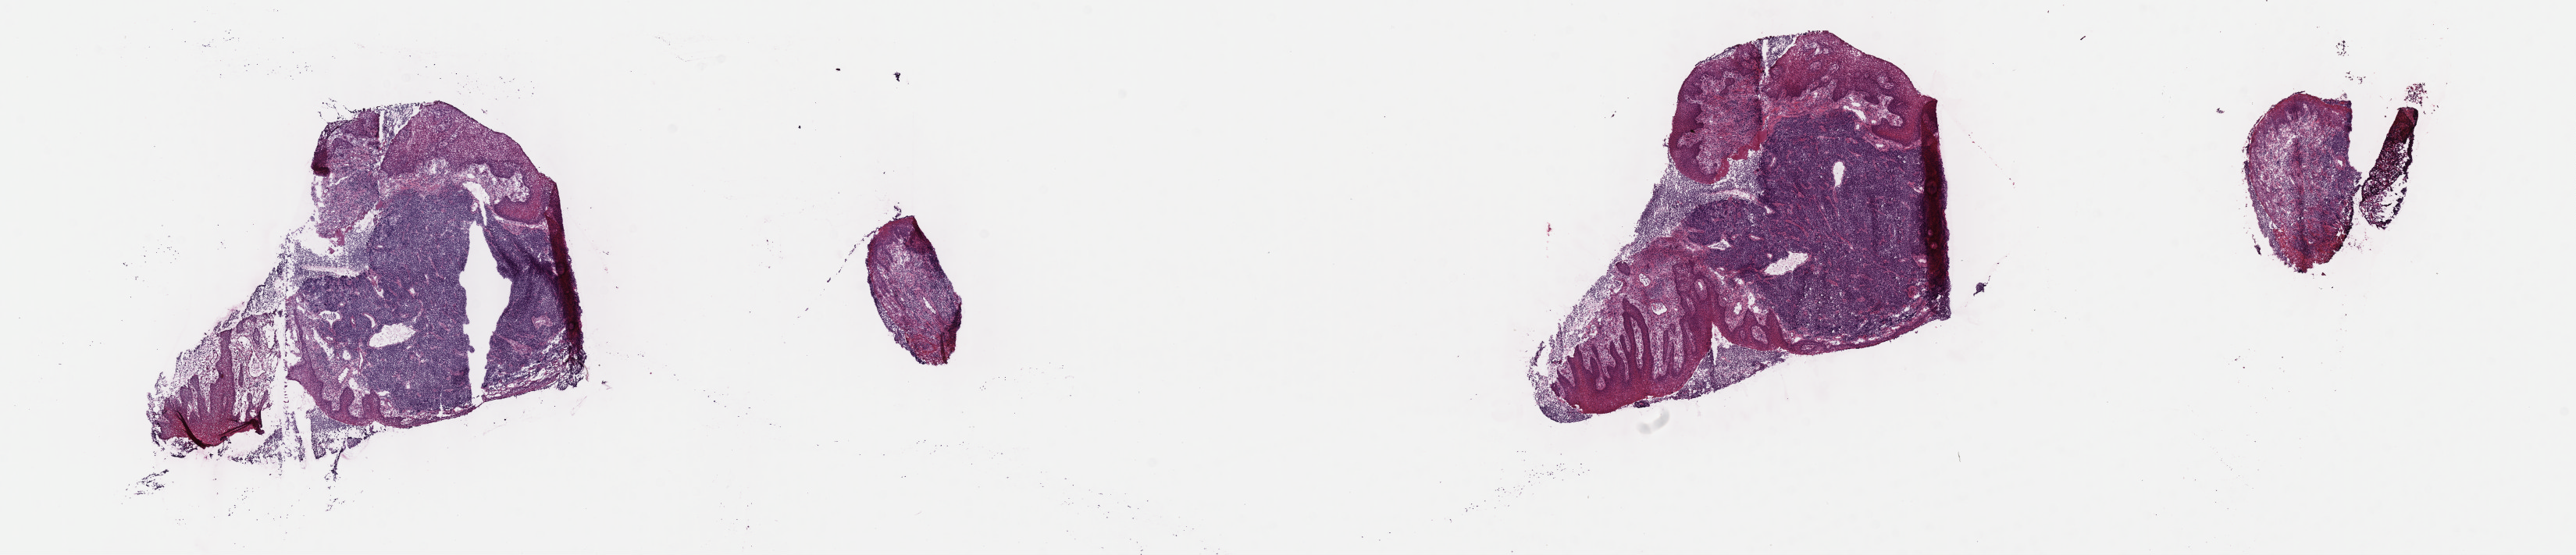
Whole-slide image, H&E stain, whole scanned area (about 26.7 x 5.7 mm) shown as a low-resolution overview, cryosection, primary tumor, site: mandible. Patient: male, age at initial diagnosis 4 years. Composition of this section per pathologist review: tumor cells 95%, tumor nuclei 90%, stromal cells 3%, necrosis 2%, normal cells 0%. Inflammatory infiltration, as recorded: lymphocyte infiltration 3%, monocyte infiltration 5%, neutrophil infiltration 0%.
Ann Arbor stage (patient): Stage I. Histologic diagnosis: Burkitt lymphoma, NOS. Section: bottom of the tissue portion.